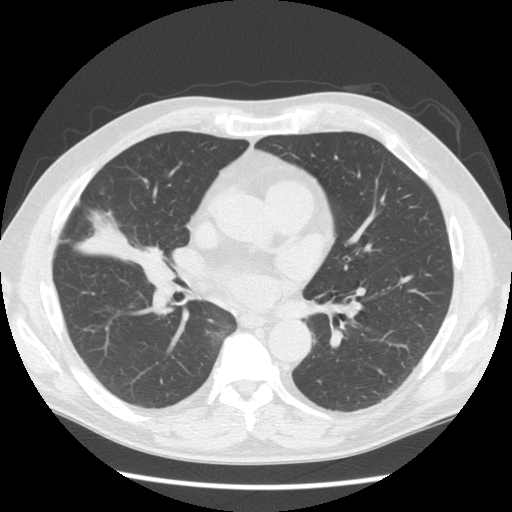
Low-dose screening chest CT, one axial slice; position 77 of 146 along the scan axis; reconstruction kernel STANDARD; 120 kVp; lung window (W 1500 / L -600 HU); 2.5 mm slice thickness; 512 × 512 image matrix, field of view 350 × 350 mm.
Outlined on this slice (manually delineated by an expert):
- lesion 1 (tumor, middle lobe of right lung): bounding box <80,236,107,253> (left, top, right, bottom; pixels)